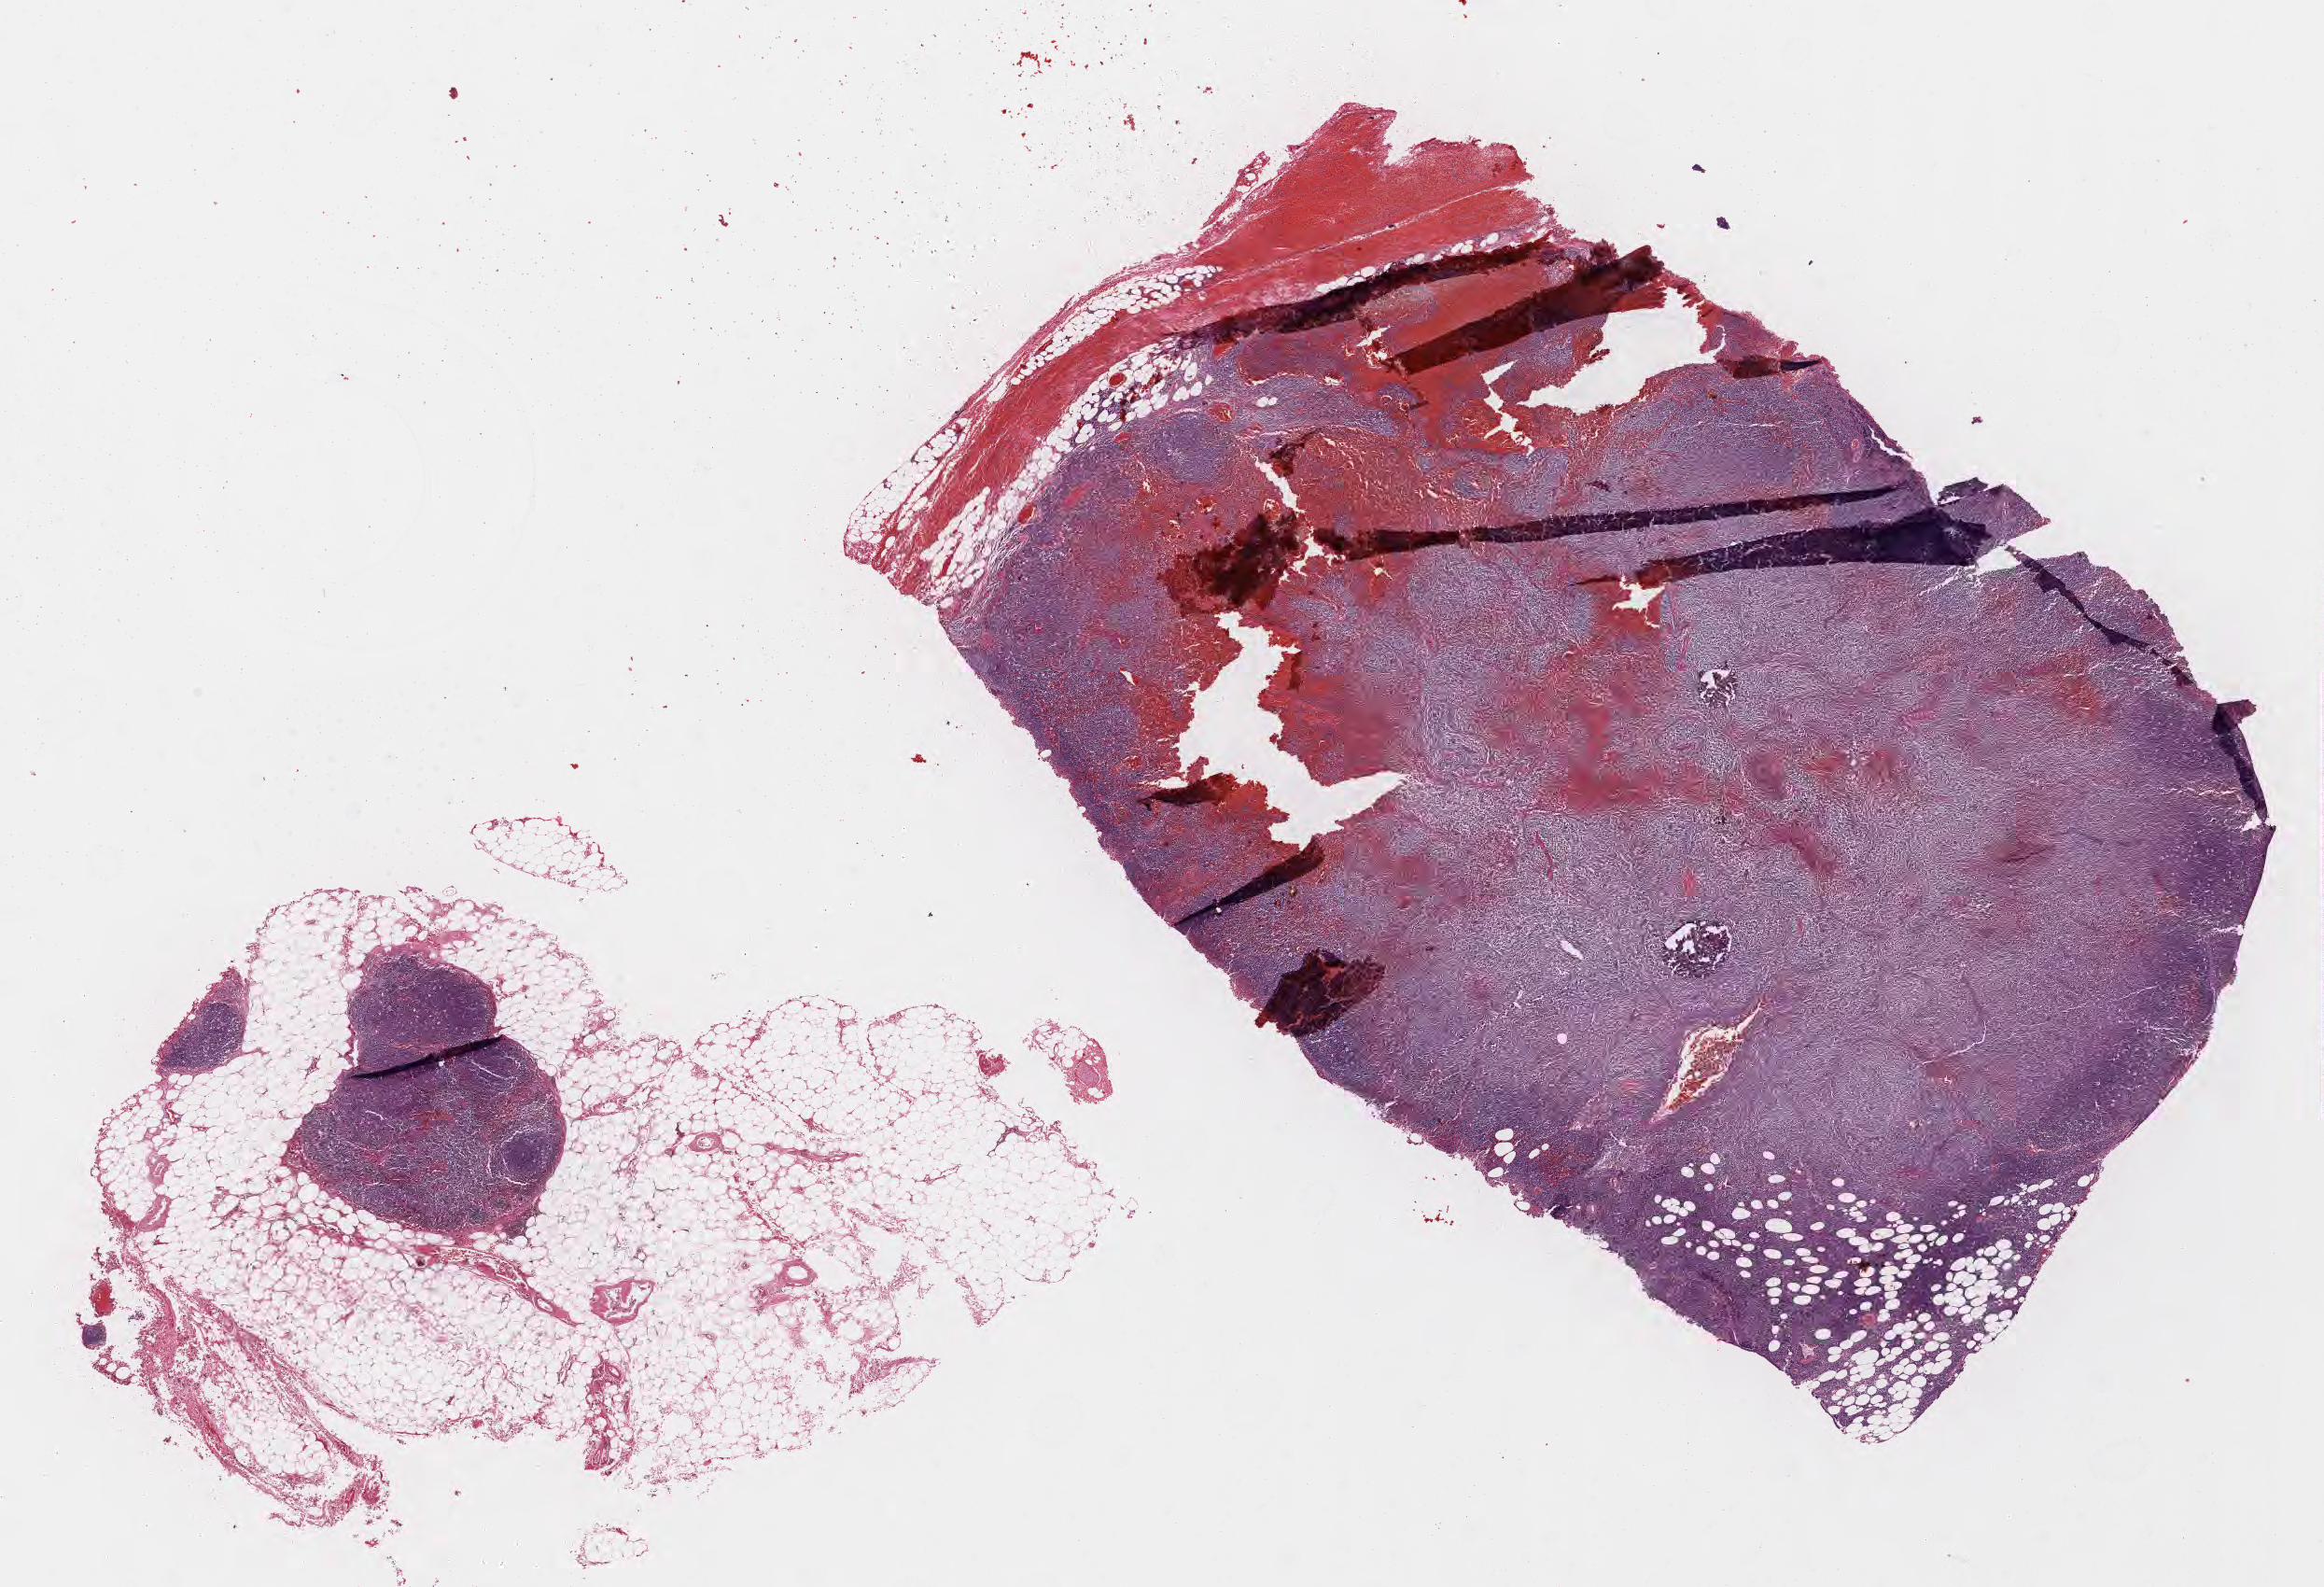
Digitized haematoxylin and eosin-stained section — shown as a low-resolution overview of the whole scanned area (about 20.1 x 13.7 mm); tumor tissue. Patient male; age 40 years.
Diagnosis: Burkitt lymphoma, NOS.